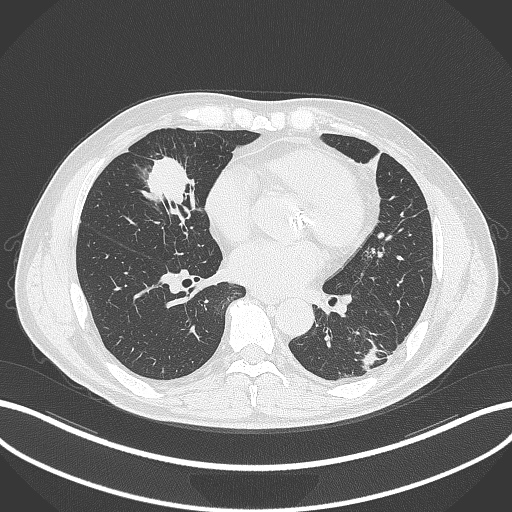
Chest CT, one axial slice; position 123 of 399 along the scan axis; reconstruction kernel B70f; 120 kVp; lung window (W 1500 / L -600 HU); 512 × 512 image matrix, field of view 400 × 400 mm. Male patient, age 59 years. Case-level facts recorded for this patient, not image findings: clinical TNM (as recorded): T2a N1 M0.
Annotated regions visible in this slice (rectangle marked by the reading radiologist):
- lung tumour (recorded histology: adenocarcinoma): bounding box (x1, y1, x2, y2) in pixels: (139, 152, 201, 224)